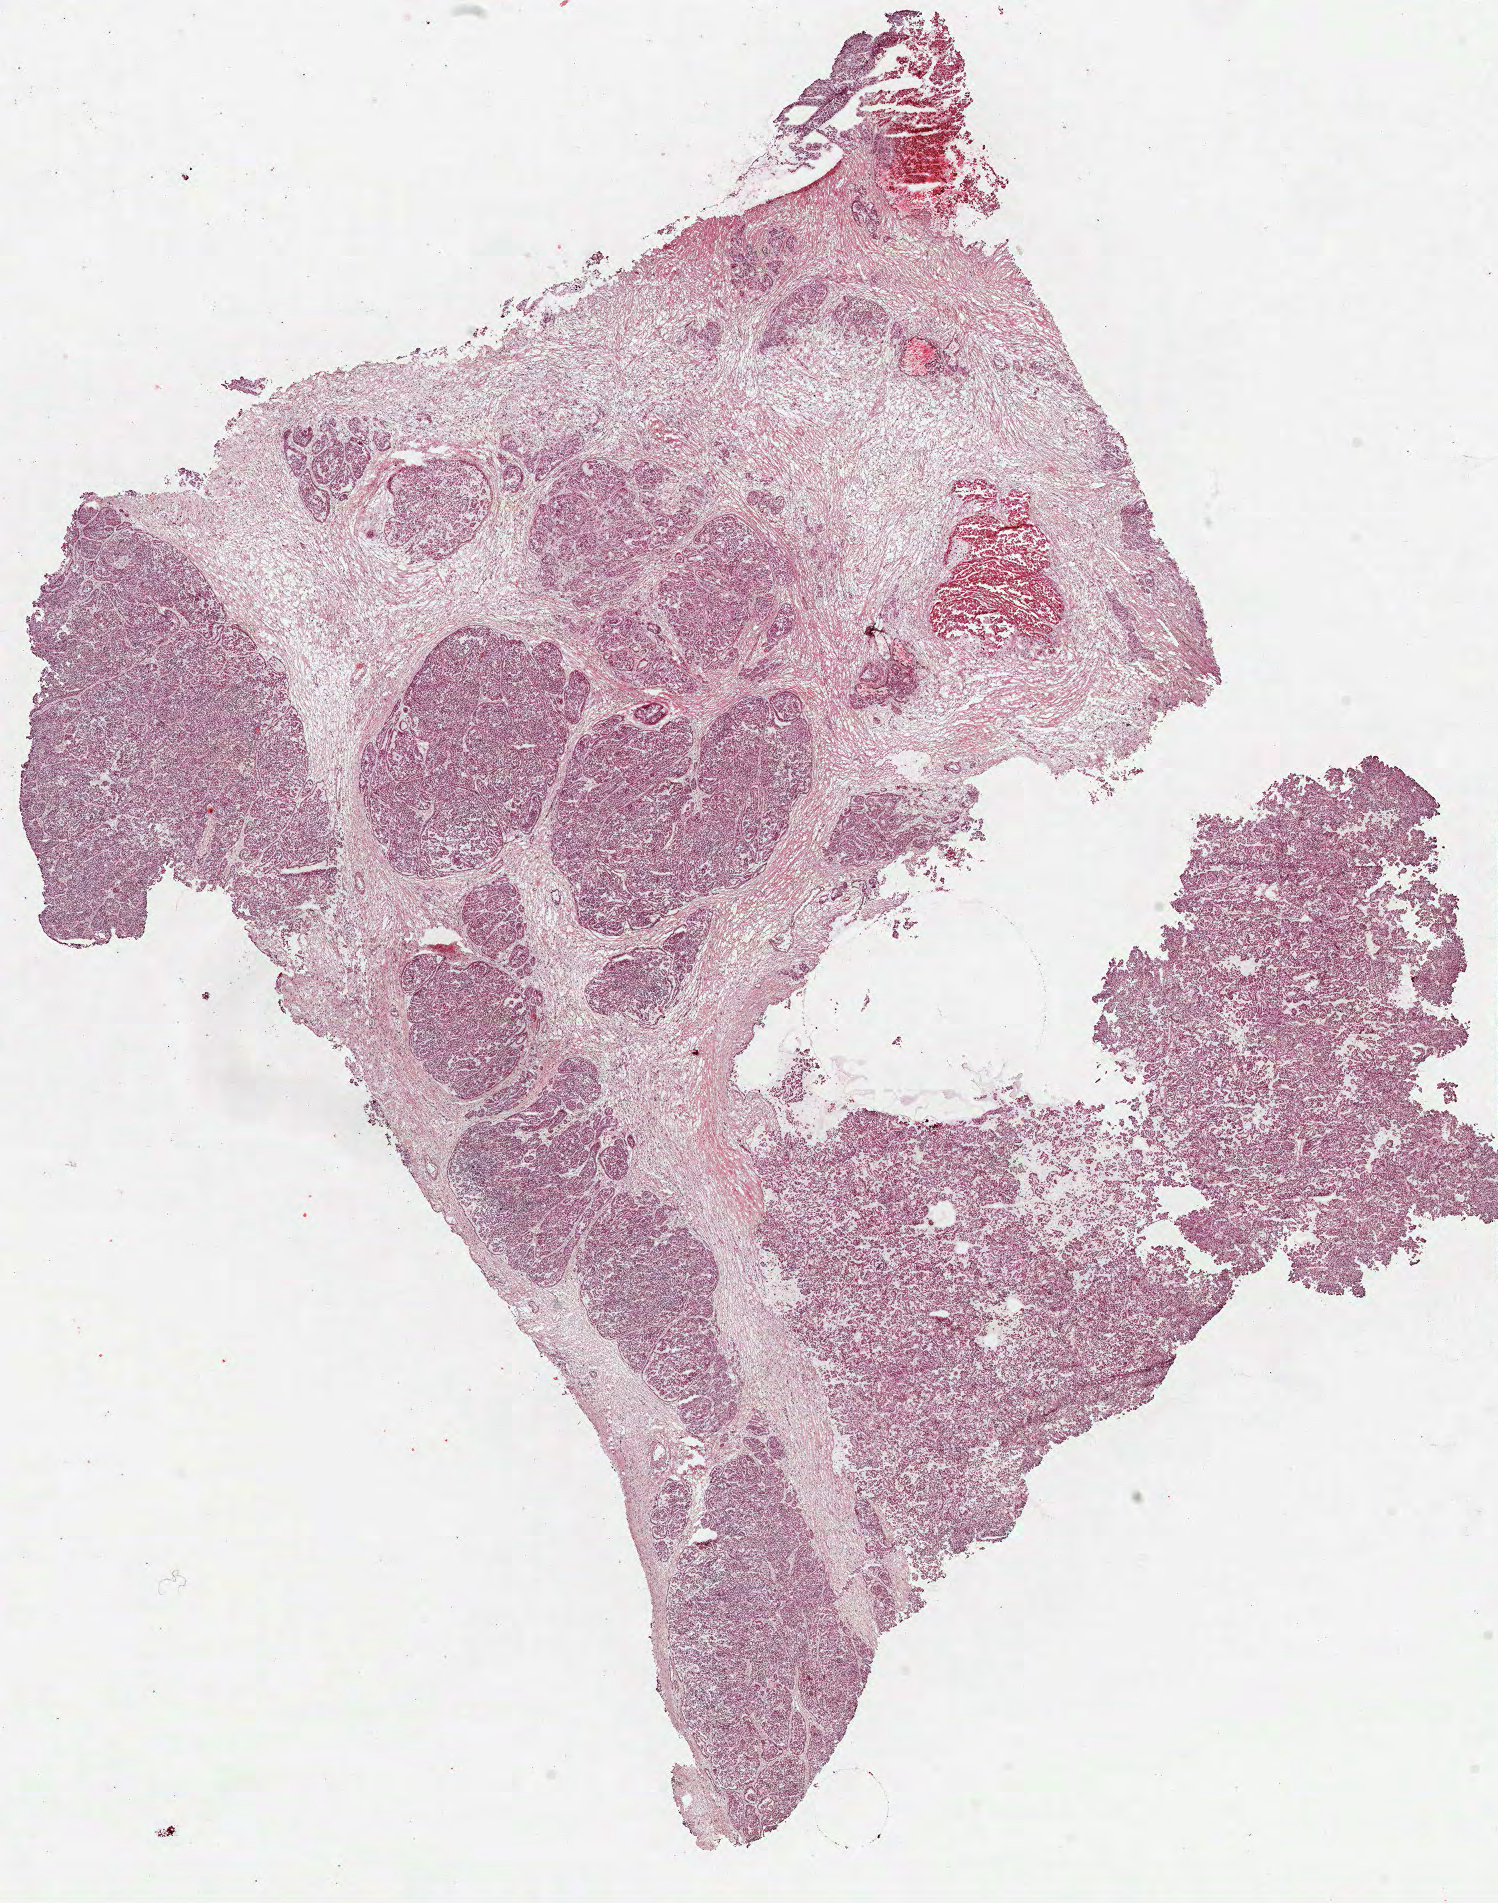
Whole-slide histology image, H&E-stained, a low-resolution overview of the entire scanned area, about 12.1 x 15.4 mm (from a 40x scan); frozen section from the top of the tissue portion; kidney, primary tumour sample. Patient: female, age at initial diagnosis 75 years. Slide review estimates, as recorded: tumour cells 80%, tumour nuclei 85%, normal cells 0%, stromal cells 15%, necrosis 5%. Inflammatory infiltration, as recorded: lymphocyte infiltration 3%, monocyte infiltration 2%, neutrophil infiltration 0%.
- histologic diagnosis: Papillary adenocarcinoma, NOS
- AJCC pathologic stage: III (6th edition)
- laterality: right
- lymph nodes positive (case pathology): 0 of 11 examined